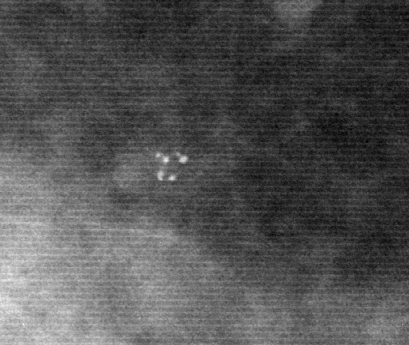
Crop from a digitized film mammogram around one marked abnormality; left breast; CC view; BI-RADS breast density category 2 (scale 1–4).
Marked abnormality: calcifications, morphology punctate, distribution clustered; BI-RADS assessment category 3; pathology result (as recorded, not read from the image): benign.